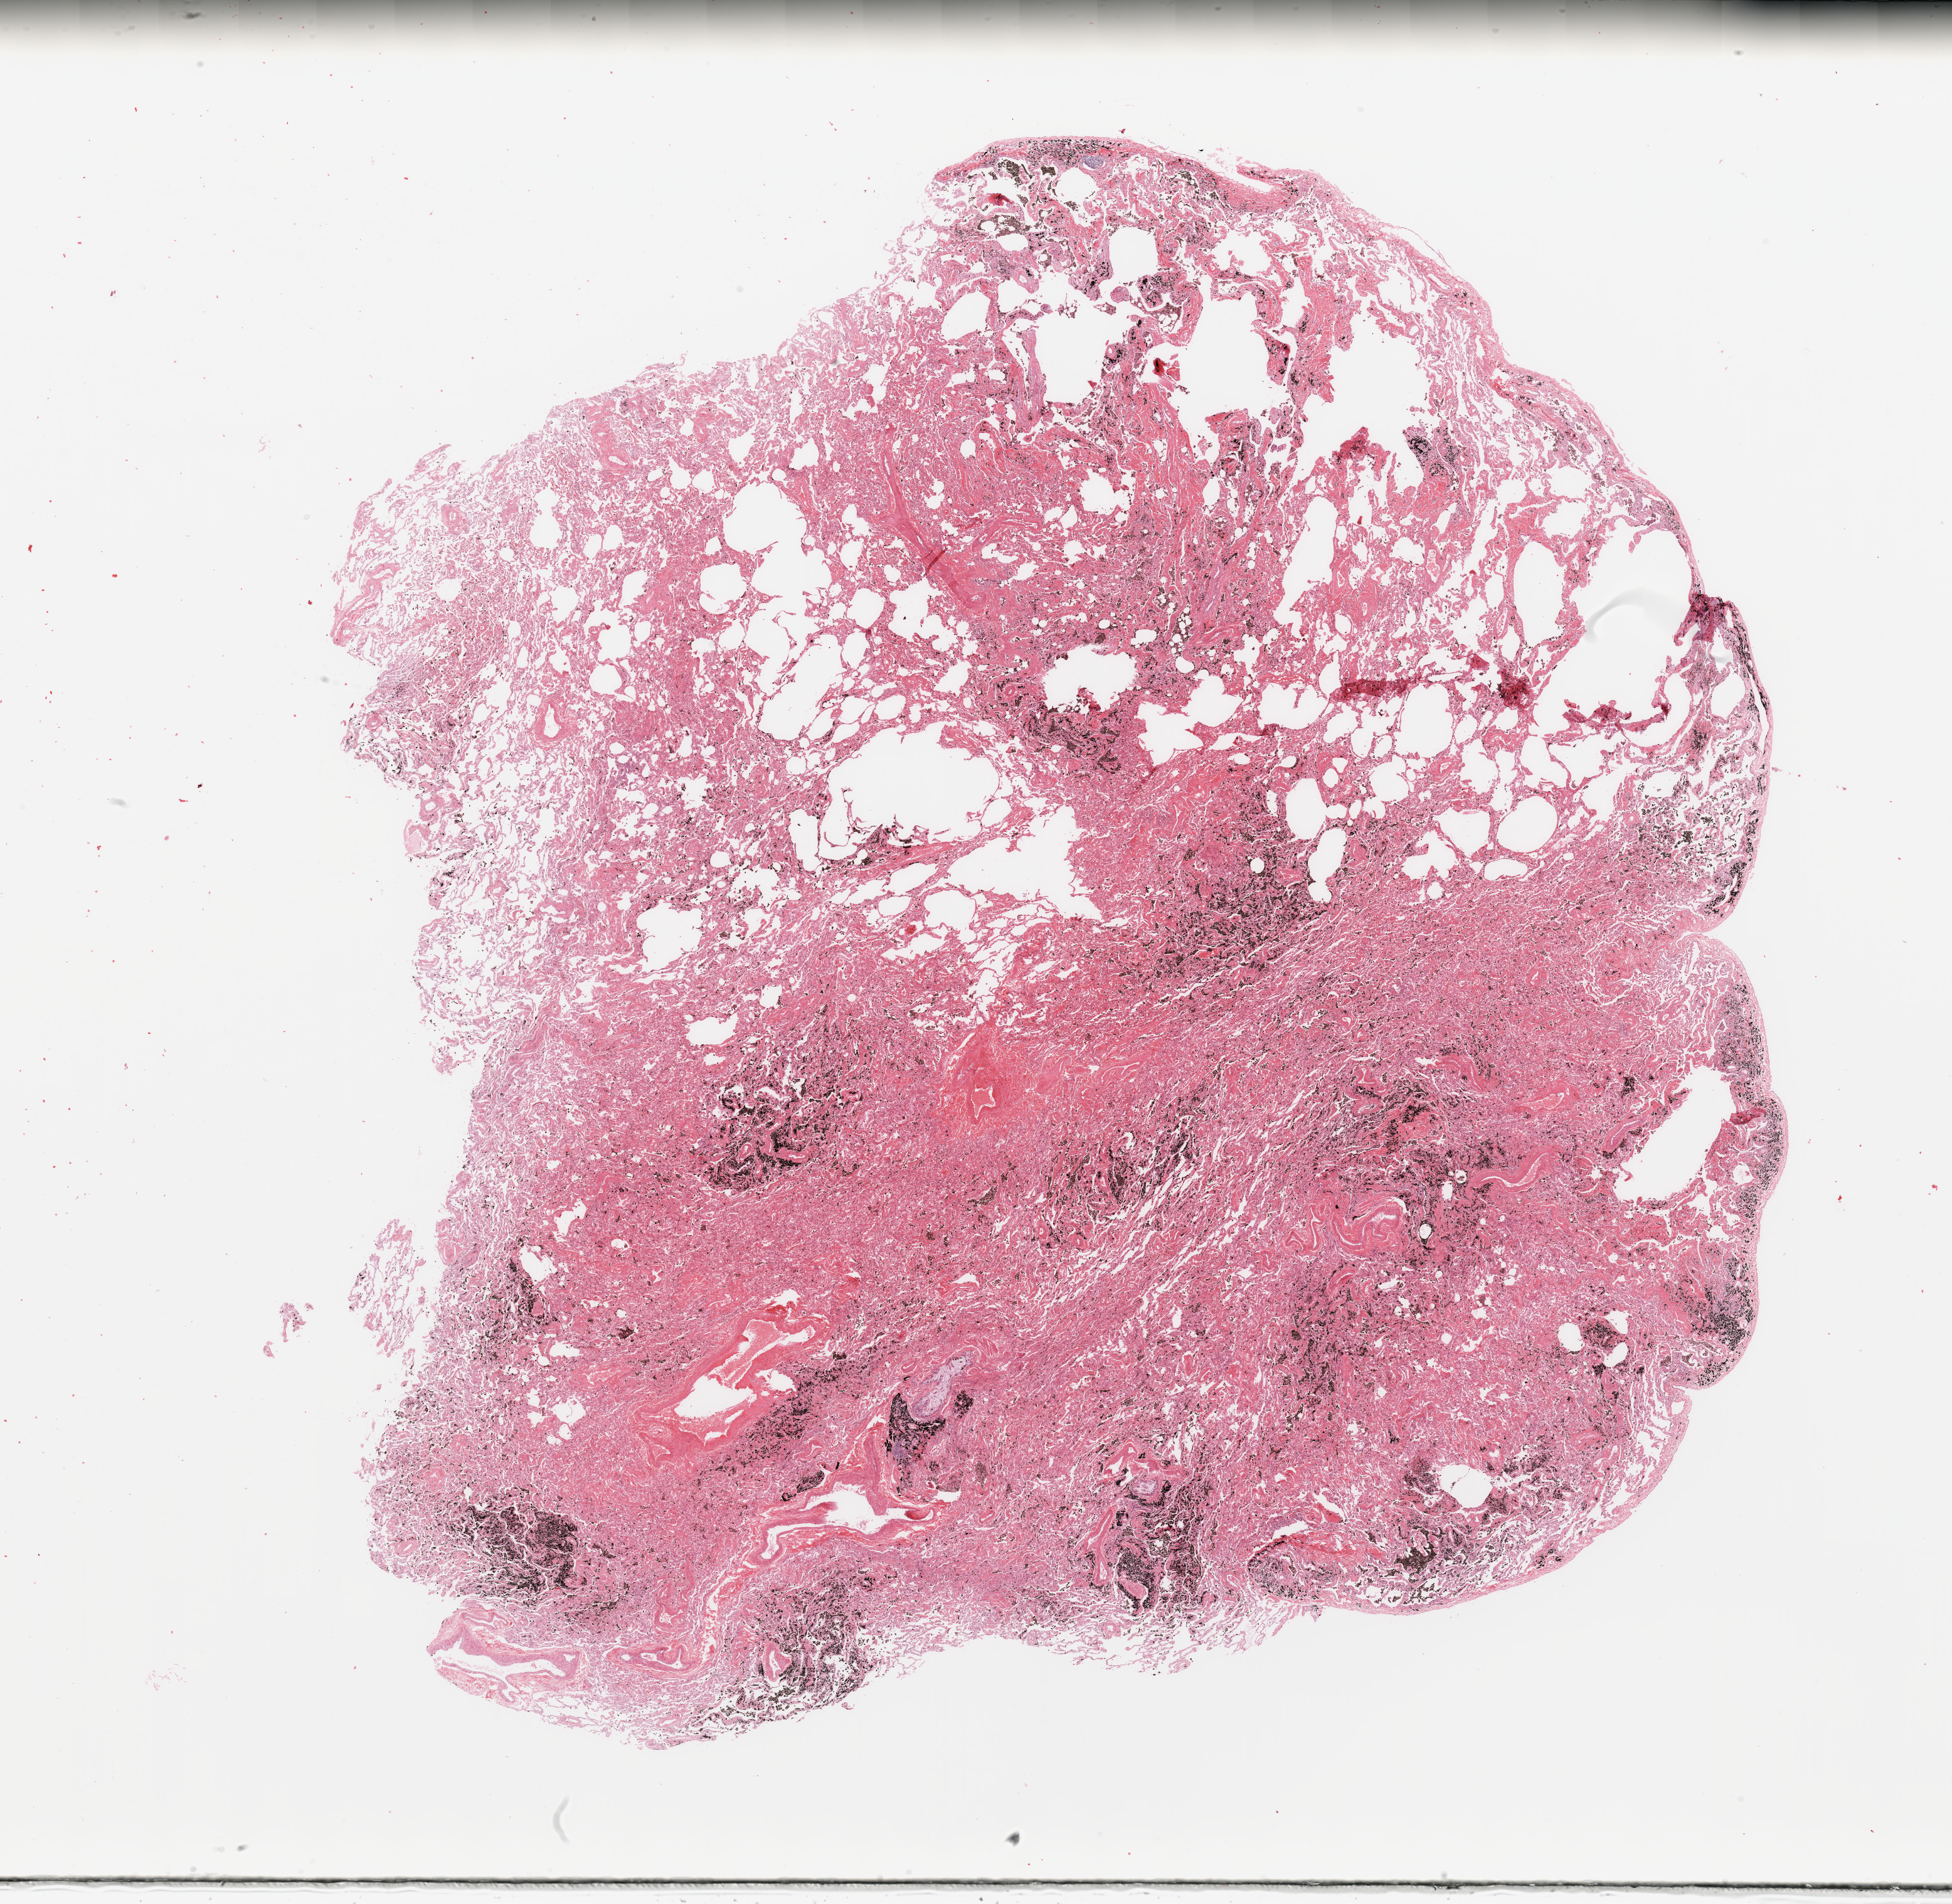
Digitized H&E-stained tissue section (whole slide), low-resolution overview of the scanned area, about 24.6 x 24.0 mm, normal (non-tumour) tissue sample, sampled site: lung. 65-year-old male patient.
This section: normal (non-tumour) tissue from the same patient. Patient diagnosis: Squamous cell carcinoma, NOS.